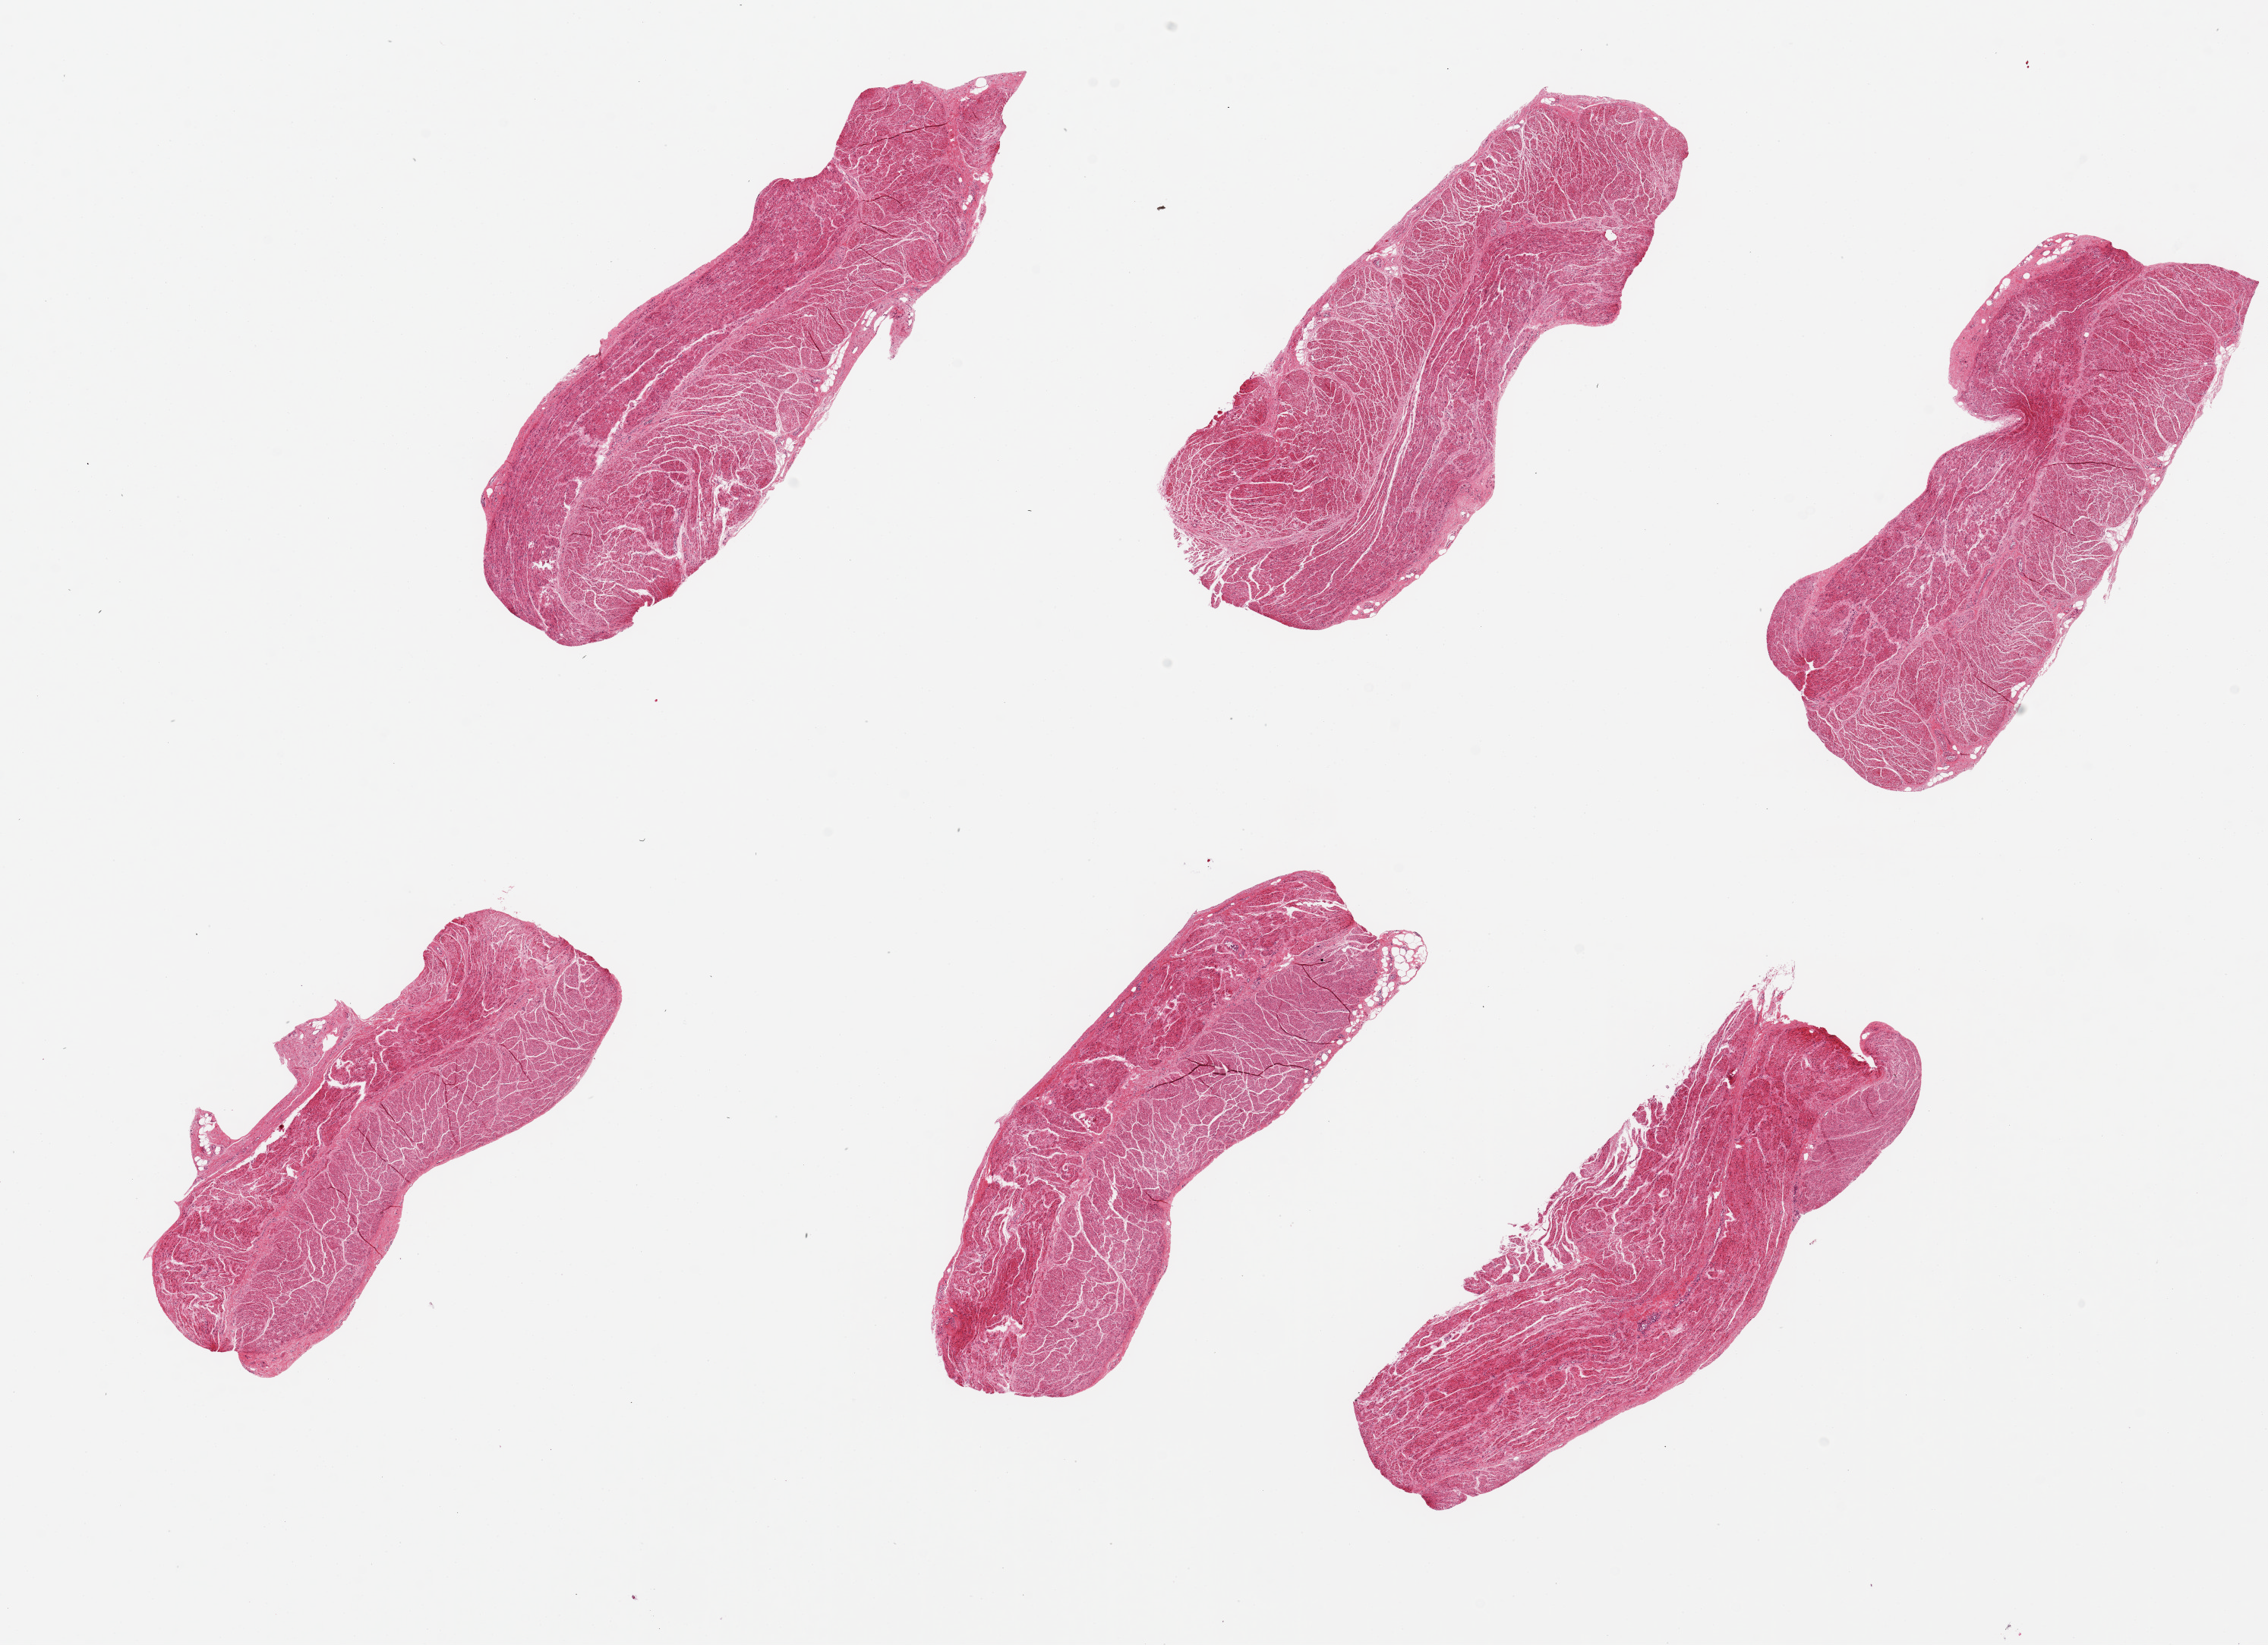
Whole-slide image, hematoxylin and eosin (H&E) stain — shown as a low-resolution overview of the whole scanned area (about 23.6 x 17.1 mm); PAXgene-fixed, paraffin-embedded tissue; section of gastroesophageal junction (target tissue); donor tissue sample. Donor sex: male.
Reviewer comment on this tissue sample: 6 pieces all muscle ~6x2.5mm.